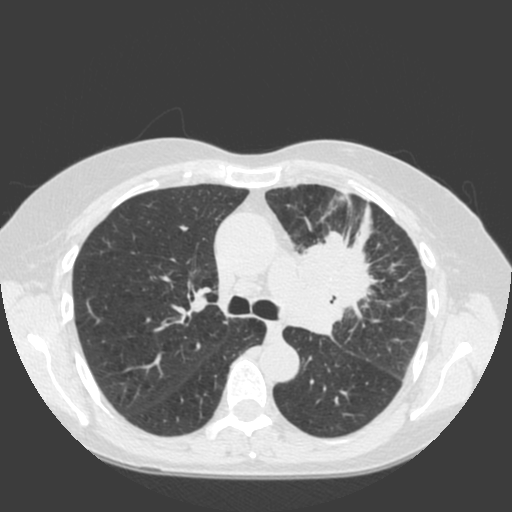
Chest CT (low-dose screening protocol), one axial image. Baseline annual screen. Lung window (W 1500 / L -600 HU). 120 kVp. Female, age 66 years at enrolment. Current smoker at enrolment.
Expert reader's lesion annotation, box from (x=281, y=221) to (x=400, y=328) px. The exam's reader record, not a measurement of the box and not confirmed to be the same lesion: non-calcified nodule or mass ≥4 mm, left upper lobe, 61 × 45 mm, spiculated (stellate) margins, soft tissue attenuation. Later outcome: lung cancer diagnosed 19 days after this screen — squamous cell carcinoma, keratinizing, NOS, left upper lobe, left hilum, mediastinum, left main stem bronchus, other location, poorly differentiated (G3), stage IIIB (AJCC 6th edition), 60 mm at pathology.